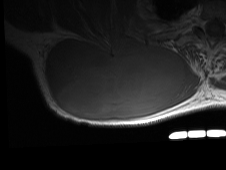
MRI of an extremity soft-tissue mass, one axial slice. Position 42 of 81 along the scan axis. MR volume resampled by the dataset authors to the PET/CT grid (not the native acquisition matrix). 3.27 mm slice thickness. 226 × 170 image matrix, field of view 221 × 166 mm. Male patient. Case-level facts recorded for this patient, not image findings: histological type: pleiomorphic spindle cell undifferentiated; grade: high; site of the primary tumour: right parascapusular.
Outlined on this slice (expert contour drawn on MRI and transferred to this co-registered scan by the dataset authors):
- gross tumour volume including surrounding oedema: bounding box [x1, y1, x2, y2] px = [44, 35, 198, 121]
- gross tumour volume (mass): [44, 40, 184, 121]